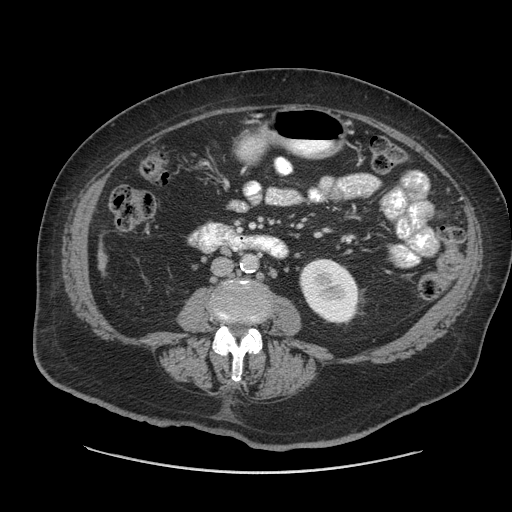
Contrast-enhanced abdominal CT (liver protocol), one axial slice; 140 kVp; soft-tissue window (W 400 / L 40 HU); 2.5 mm slice thickness; 512 × 512 image matrix, field of view 420 × 420 mm. From the clinical record (not read from this slice): diagnosis: hepatocellular carcinoma (patient treated with transarterial chemoembolisation; whether this scan precedes or follows treatment is not stated here); TNM stage (as recorded): Stage-I; Child-Pugh class: A; tumour differentiation: well differentiated.
Annotated regions visible in this slice (semi-automatic segmentation, software-assisted and operator-edited):
- liver parenchyma outside the tumour (the mass and vessels are separate outlines, so this box may not span the whole liver): bounding box (x1, y1, x2, y2) in pixels: (98, 247, 106, 272)